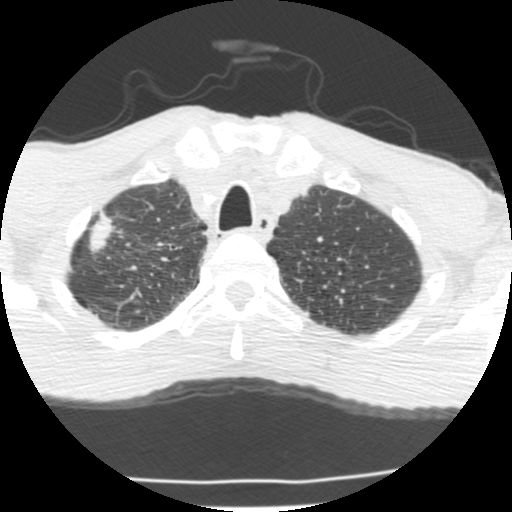
Low-dose screening chest CT, one axial slice. Slice 182 of 214 in the series (ordered by position). 120 kVp. Lung window (W 1500 / L -600 HU). 2.5 mm slice thickness. 512 × 512 image matrix, field of view 283 × 283 mm.
Outlined on this slice (outlined manually by an expert reader):
- lesion 1 (tumor, upper lobe of right lung): bounding box <89,212,116,253> (left, top, right, bottom; pixels)